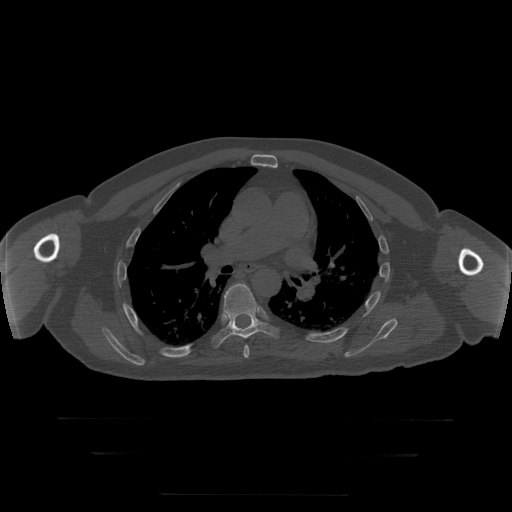
CT including the spine, one axial slice. Position 191 of 397 along the scan axis. 120 kVp. Bone window (W 1800 / L 400 HU). 1.25 mm slice thickness. 512 × 512 image matrix, field of view 510 × 510 mm. Patient age 73 years. From the clinical record (not read from this slice): primary cancer: prostate.
Annotated regions visible in this slice (semi-automatic segmentation, software-assisted and operator-edited):
- T6 vertebra: bounding box (x1, y1, x2, y2) in pixels: (244, 346, 250, 358)
- T7 vertebra: (212, 284, 279, 348)